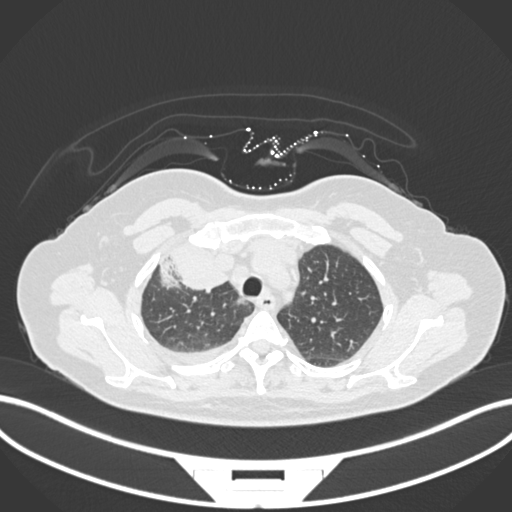
Chest CT, one axial slice; slice 130 of 172 in the series (ordered by position); reconstruction kernel B30f; 120 kVp; lung window (W 1500 / L -600 HU); 1 mm slice thickness; 512 × 512 image matrix. Female patient, age 52 years. From the clinical record (not read from this slice): clinical TNM (as recorded): T3 N1 M1.
Structures marked on this image (bounding box drawn by a radiologist):
- lung tumour (recorded histology: adenocarcinoma): bounding box (x1, y1, x2, y2) in pixels: (154, 245, 233, 292)